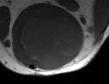
MRI of an extremity soft-tissue mass, one axial slice; position 30 of 50 along the scan axis; MR volume resampled by the dataset authors to the PET/CT grid (not the native acquisition matrix); 3.27 mm slice thickness; 109 × 84 image matrix. Male patient. Case-level facts recorded for this patient, not image findings: histological type: synovial sarcoma; site of the primary tumour: left poplietal fossa.
Structures marked on this image (expert contour drawn on MRI and transferred to this co-registered scan by the dataset authors):
- gross tumour volume (mass): bounding box [x1, y1, x2, y2] px = [16, 16, 85, 68]